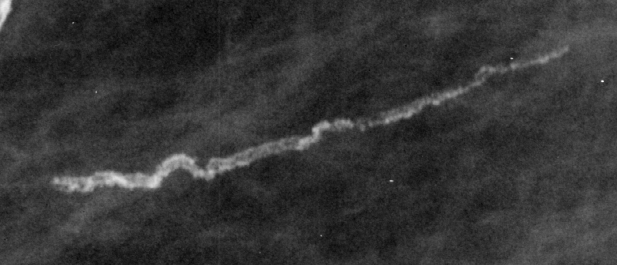
Region of interest cut from a scanned film mammogram (one marked finding), right breast, MLO view, BI-RADS breast density category 1 (scale 1–4).
- Finding: calcifications, morphology vascular; BI-RADS assessment category 2; subtlety rating 4 on a 1 (subtle) to 5 (obvious) scale; benign; no additional work-up was recommended (benign without callback).